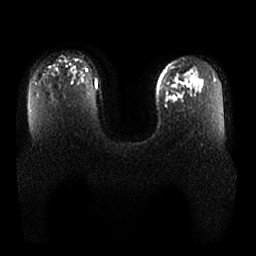
Breast MRI, one axial slice. Slice 16 of 25 in the series (ordered by position). Diffusion-weighted series; image 2 of 4 stored at this slice position (different b-values; order by instance number). 1.5 T. 4 mm slice thickness. 256 × 256 image matrix. Female patient.
Annotated regions visible in this slice (expert manual segmentation):
- tumour on diffusion-weighted imaging: bounding box <165,95,178,103> (left, top, right, bottom; pixels)